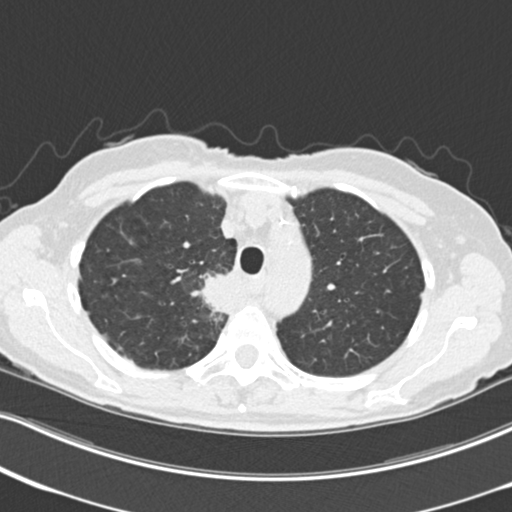
Low-dose screening chest CT, one axial slice; slice 173 of 226 in the series (ordered by position); reconstruction kernel B30f; 120 kVp; lung window (W 1500 / L -600 HU); 2 mm slice thickness; 512 × 512 image matrix, field of view 322 × 322 mm.
Outlined on this slice (manually delineated by an expert):
- lesion 1 (tumor, mediastinum): box from (x=202, y=274) to (x=232, y=315) px